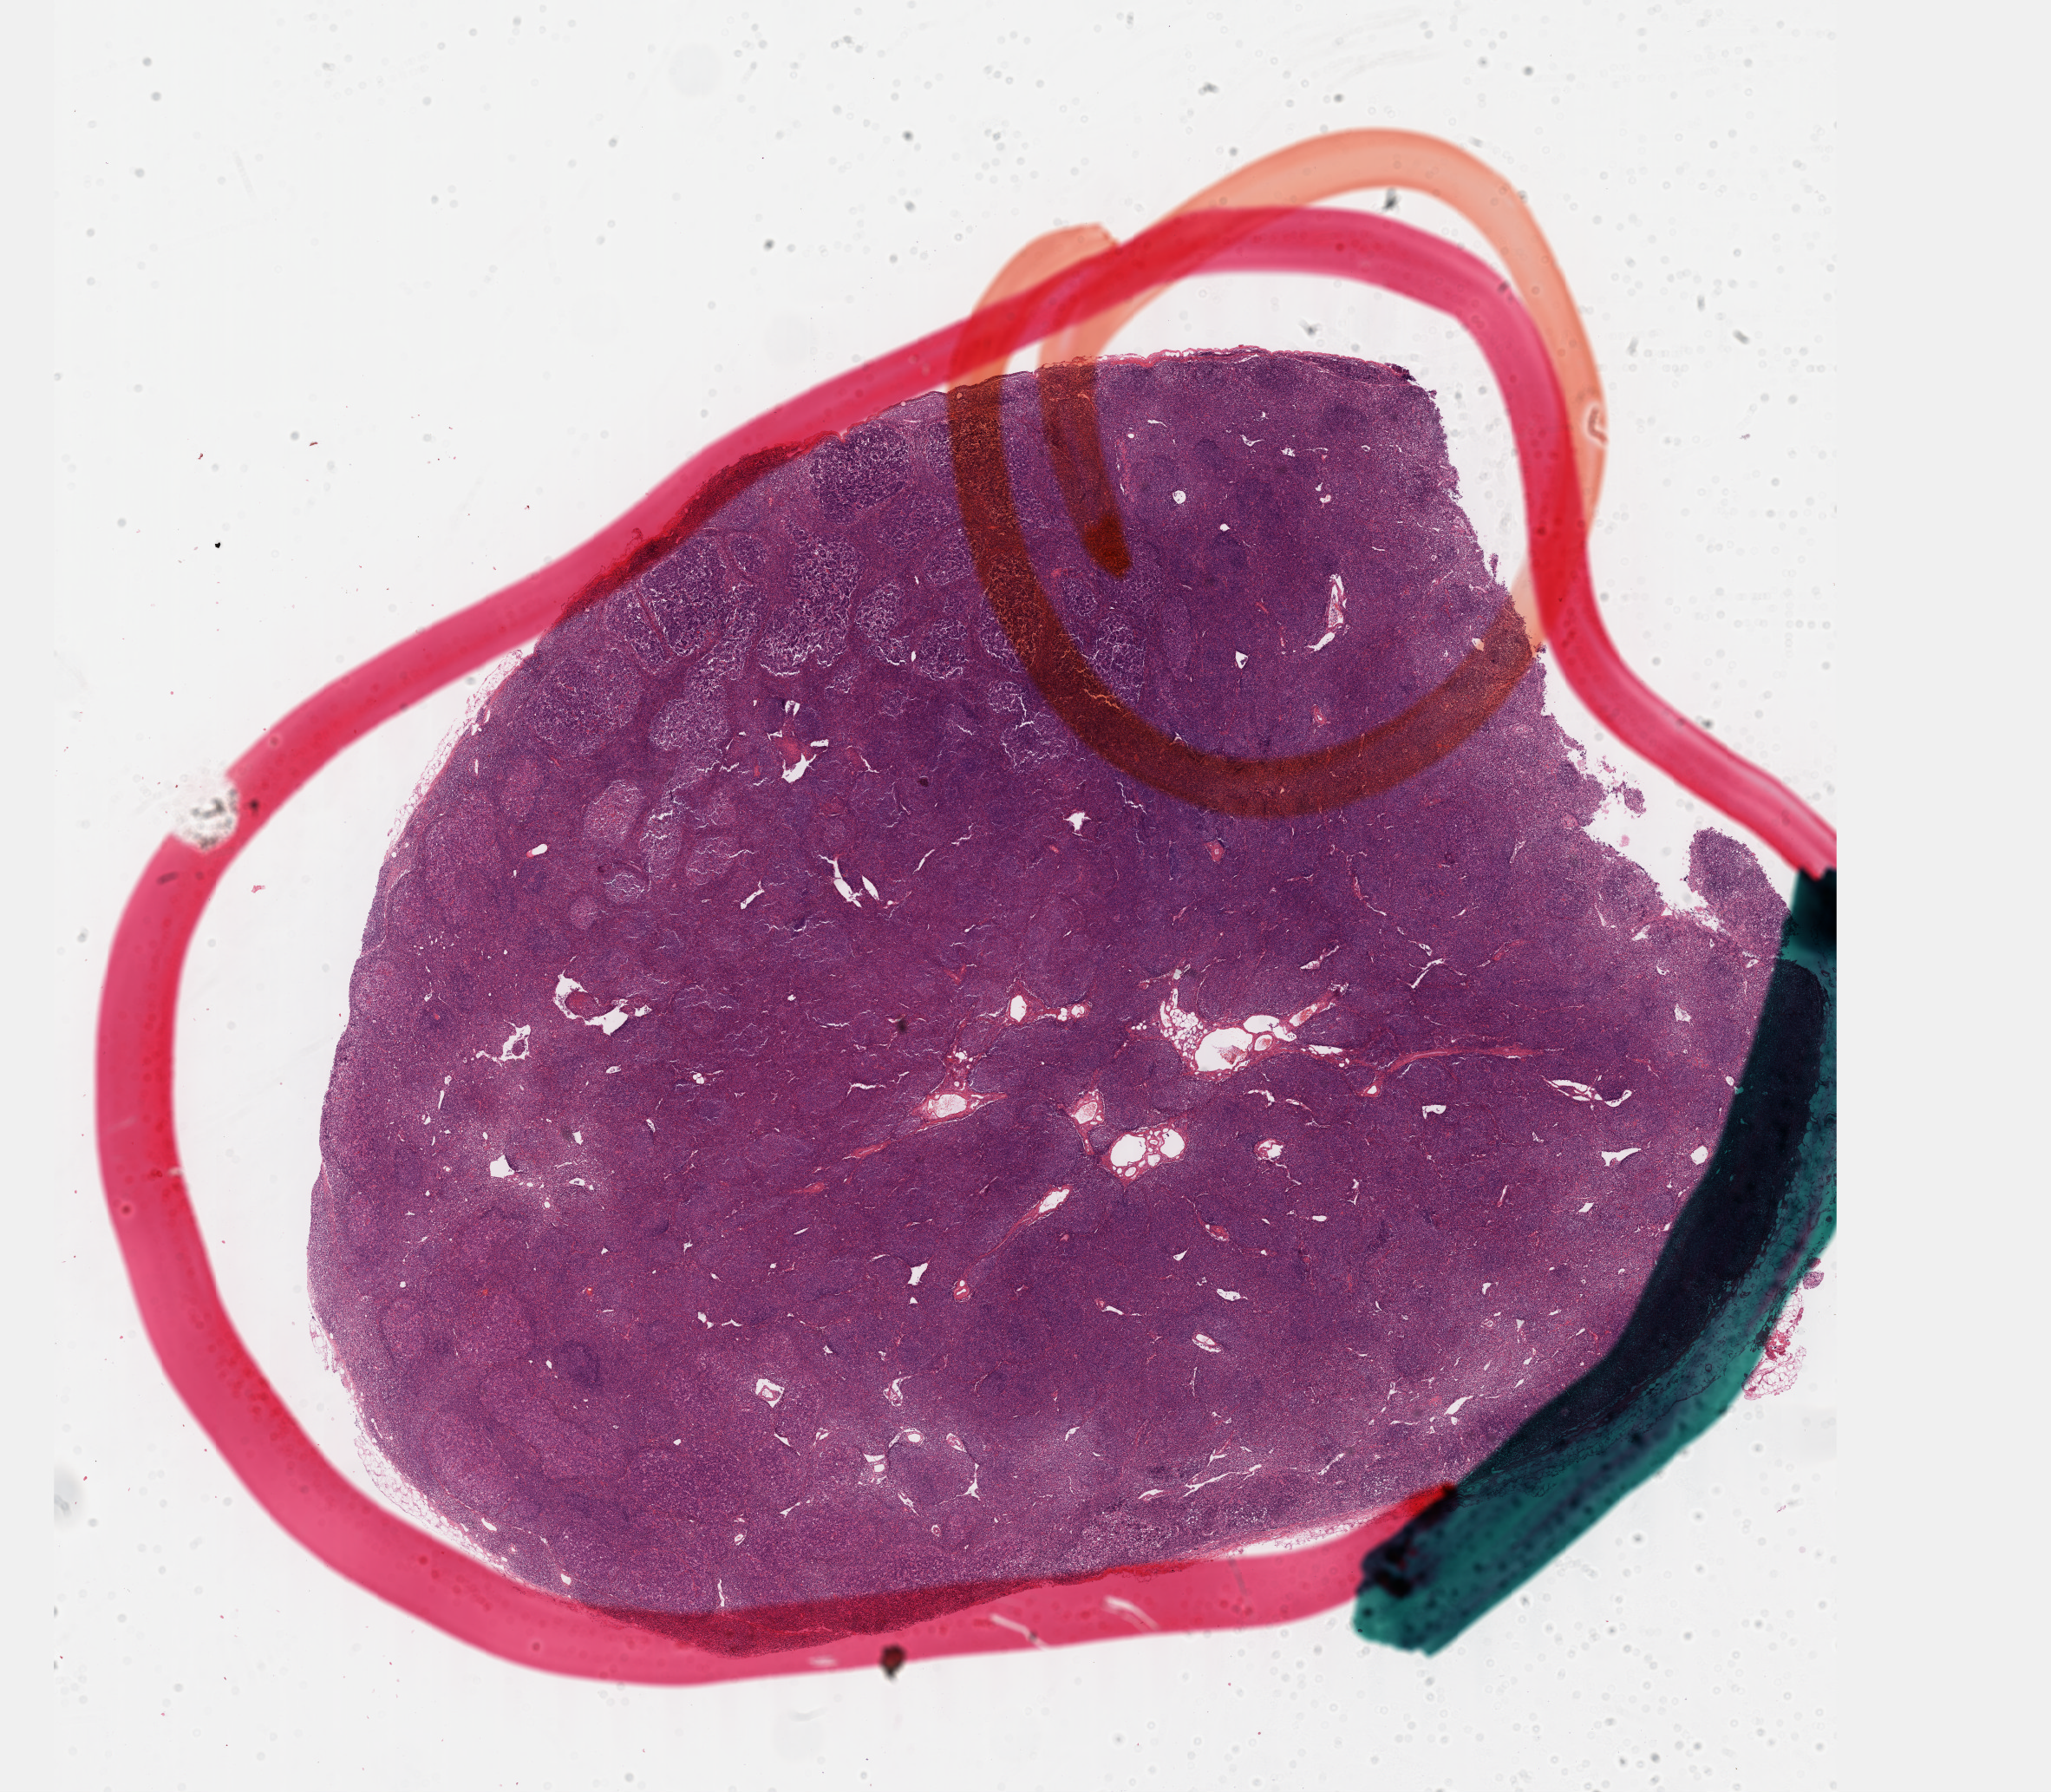
Digitized H&E tissue section (whole slide), low-resolution overview of the scanned area, about 19.1 x 16.7 mm (slide scanned at 40x), formalin-fixed paraffin-embedded (FFPE) diagnostic section, sample: primary tumour, lymphoid tissue. Patient: female, age at initial diagnosis 64 years.
Histologic diagnosis: Diffuse large B-cell lymphoma, NOS (lymph nodes of axilla or arm).